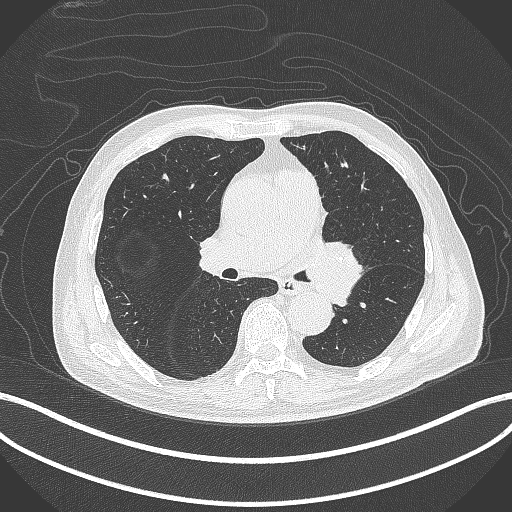
Chest CT, one axial slice. Slice 243 of 417 in the series (ordered by position). 120 kVp. Lung window (W 1500 / L -600 HU). 1 mm slice thickness. 512 × 512 image matrix, field of view 400 × 400 mm. Male patient, age 77 years. Case-level facts recorded for this patient, not image findings: clinical TNM (as recorded): T3 N1 M0.
Outlined on this slice (bounding box drawn by a radiologist):
- lung tumour (recorded histology: adenocarcinoma): bounding box (x1, y1, x2, y2) in pixels: (303, 233, 366, 308)